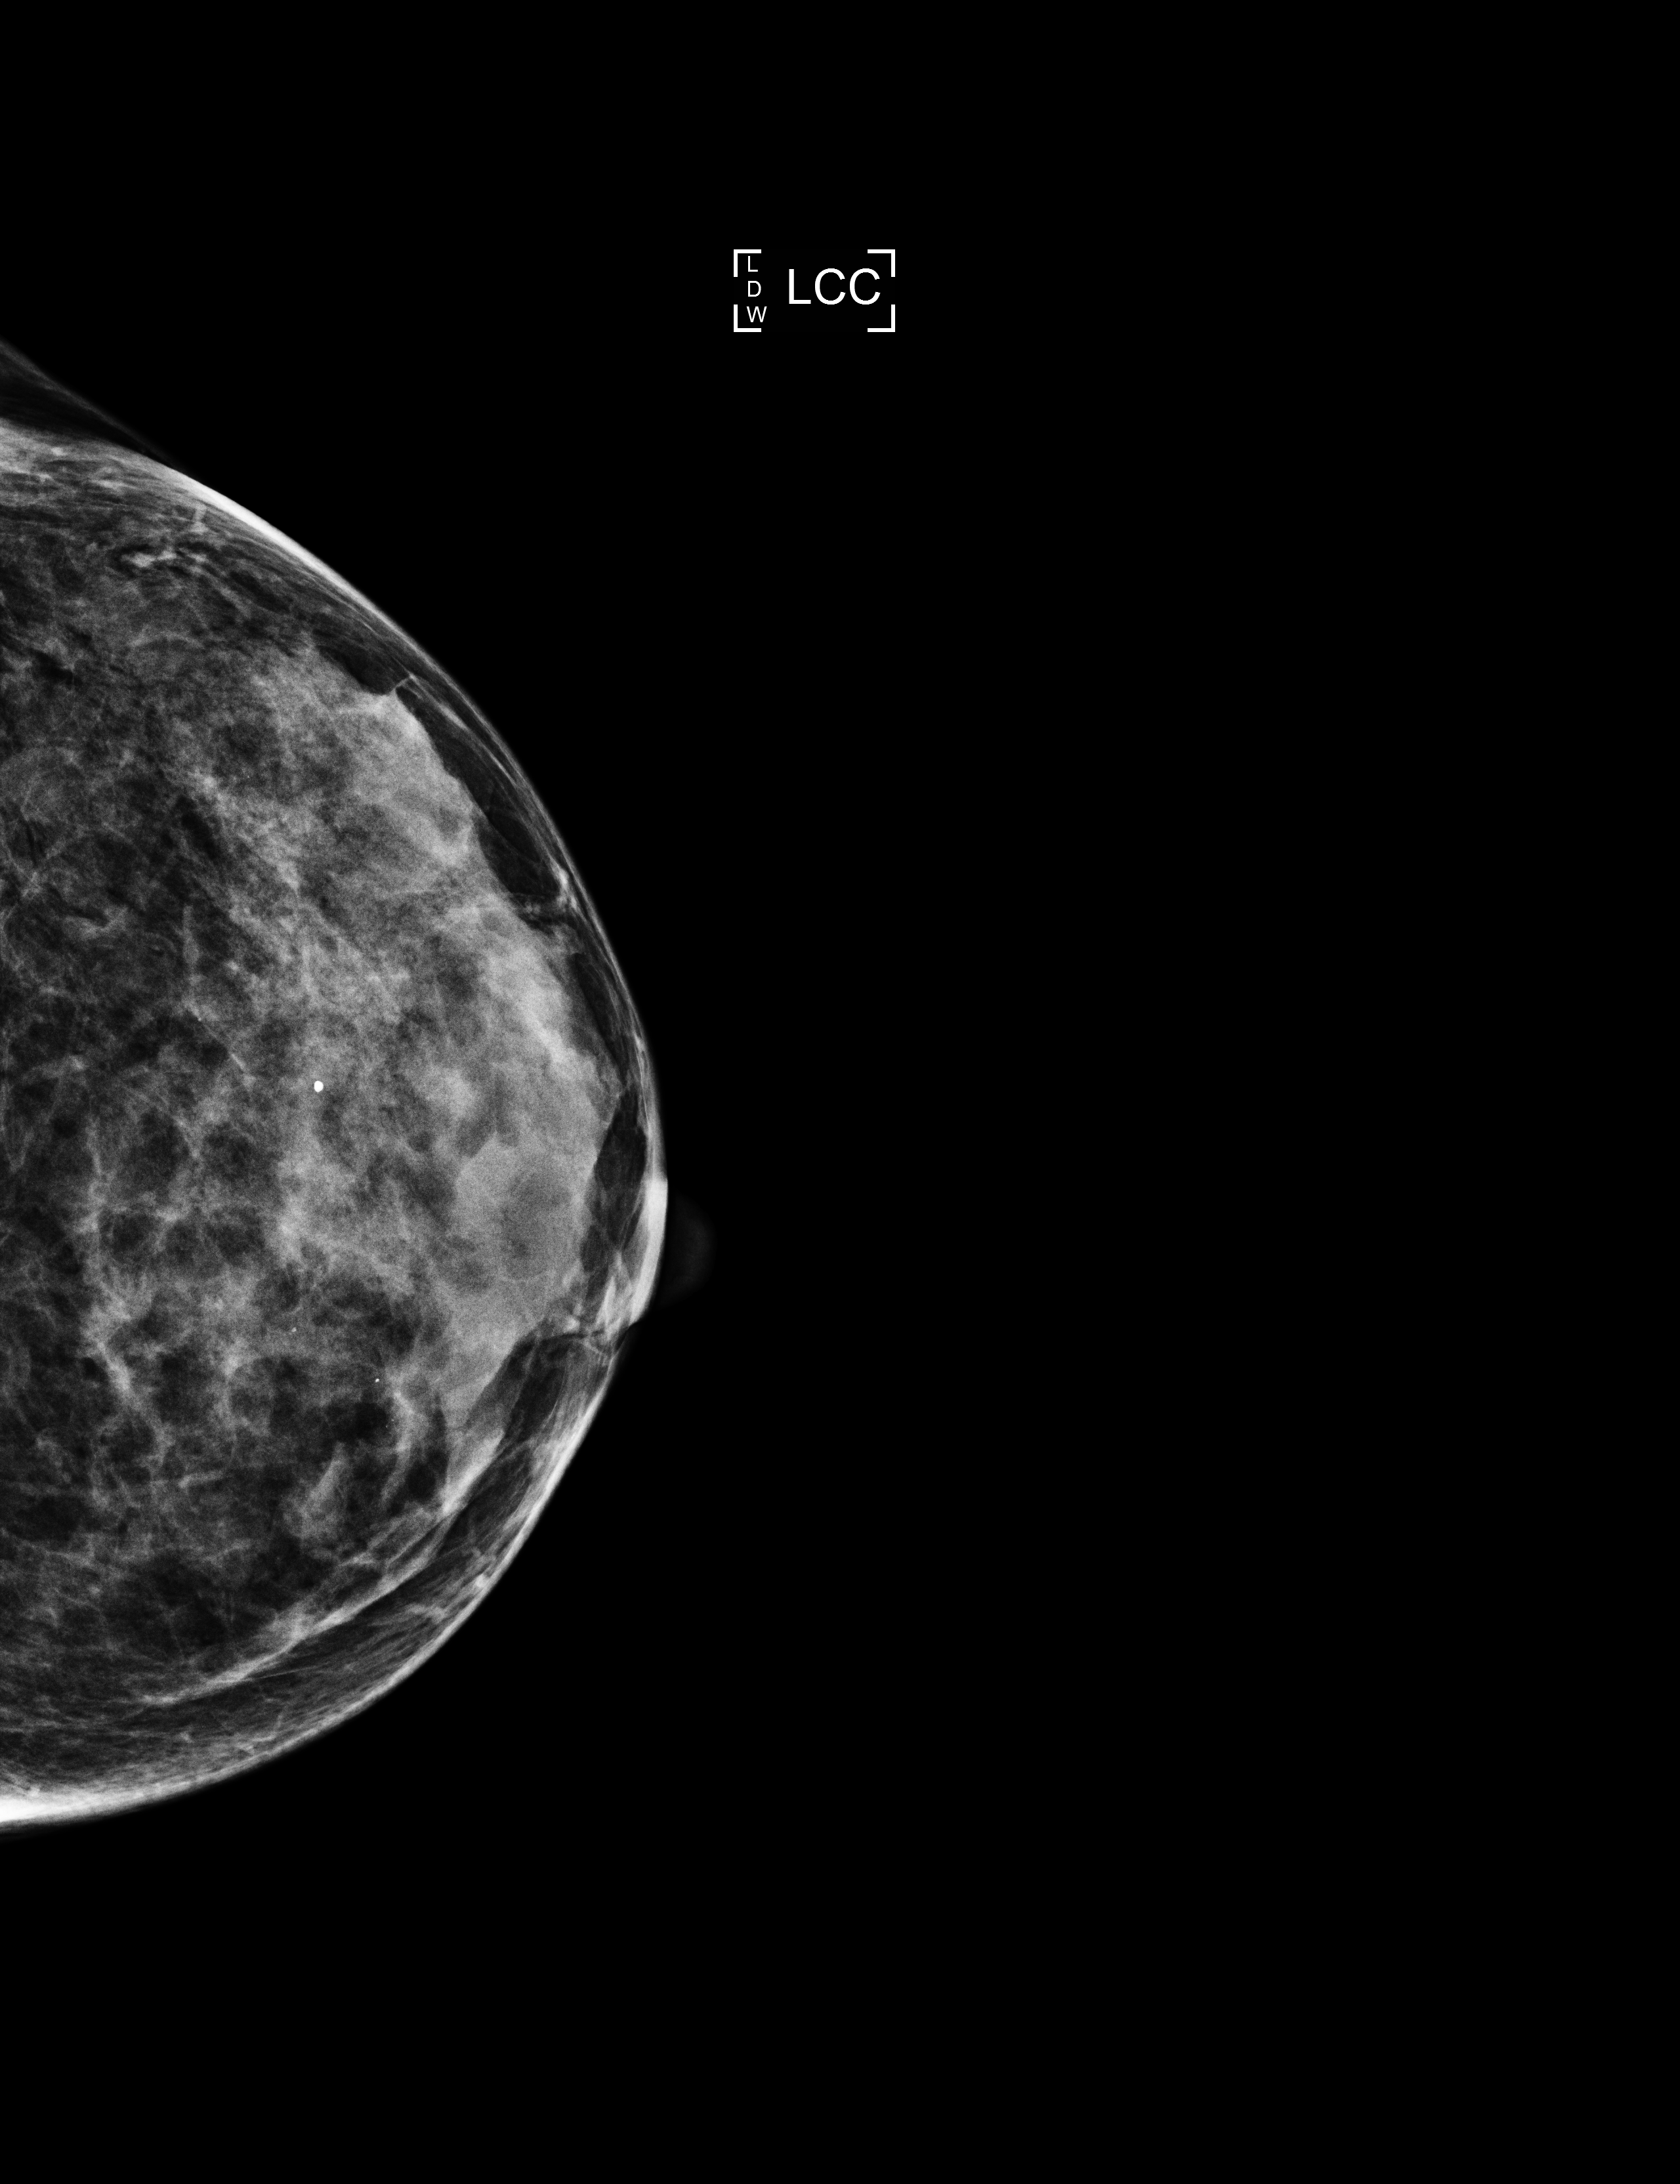
Annual screening mammography examination. Female patient, age 58 years.
Image type: full-field digital mammogram. Breast: left. Projection: cranio-caudal projection. BI-RADS breast density category at the screening exam (both breasts, scale 1–4): 3. Final BI-RADS assessment for this screening round (tomosynthesis exam, both breasts): category 2. Recall: no recall after this screen.